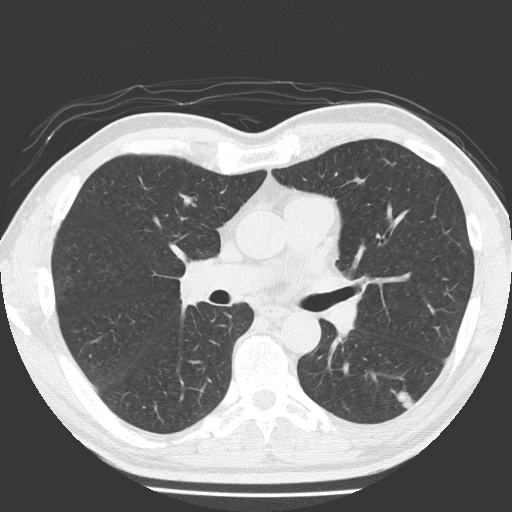
Axial slice from a low-dose chest CT screening exam. First (baseline) screen. Lung window (W 1500 / L -600 HU). Lung (sharp) reconstruction kernel (FC51). Slice 81 of 184 in the series. 512 × 512 image matrix, field of view 348 × 348 mm. Male participant, aged 58 years at enrolment. Current smoker at enrolment.
Expert reader's lesion annotation, bounding box <362,373,428,423> (left, top, right, bottom; pixels). The screening reader recorded 4 non-calcified nodules or masses ≥4 mm on this exam (left lower lobe, left lower lobe, right middle lobe, left upper lobe); which of them this box marks is not recorded. Later outcome: lung cancer diagnosed 99 days after this screen — adenosquamous carcinoma, left lower lobe, moderately differentiated (G2), stage IA (AJCC 6th edition), 28 mm at pathology.